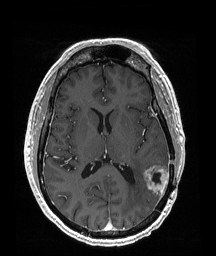
Brain MRI from a brain-tumour surgery series, one axial slice. Position 88 of 192 along the scan axis. T1-weighted post-contrast. 1 mm slice thickness. 216 × 256 image matrix, field of view 211 × 250 mm. From the clinical record (not read from this slice): histopathology: Glioblastoma; WHO grade: 4; IDH mutation: no; tumour location: Left Temporoparietal.
Annotated regions visible in this slice (expert manual segmentation):
- tumour: box from (x=144, y=166) to (x=170, y=197) px